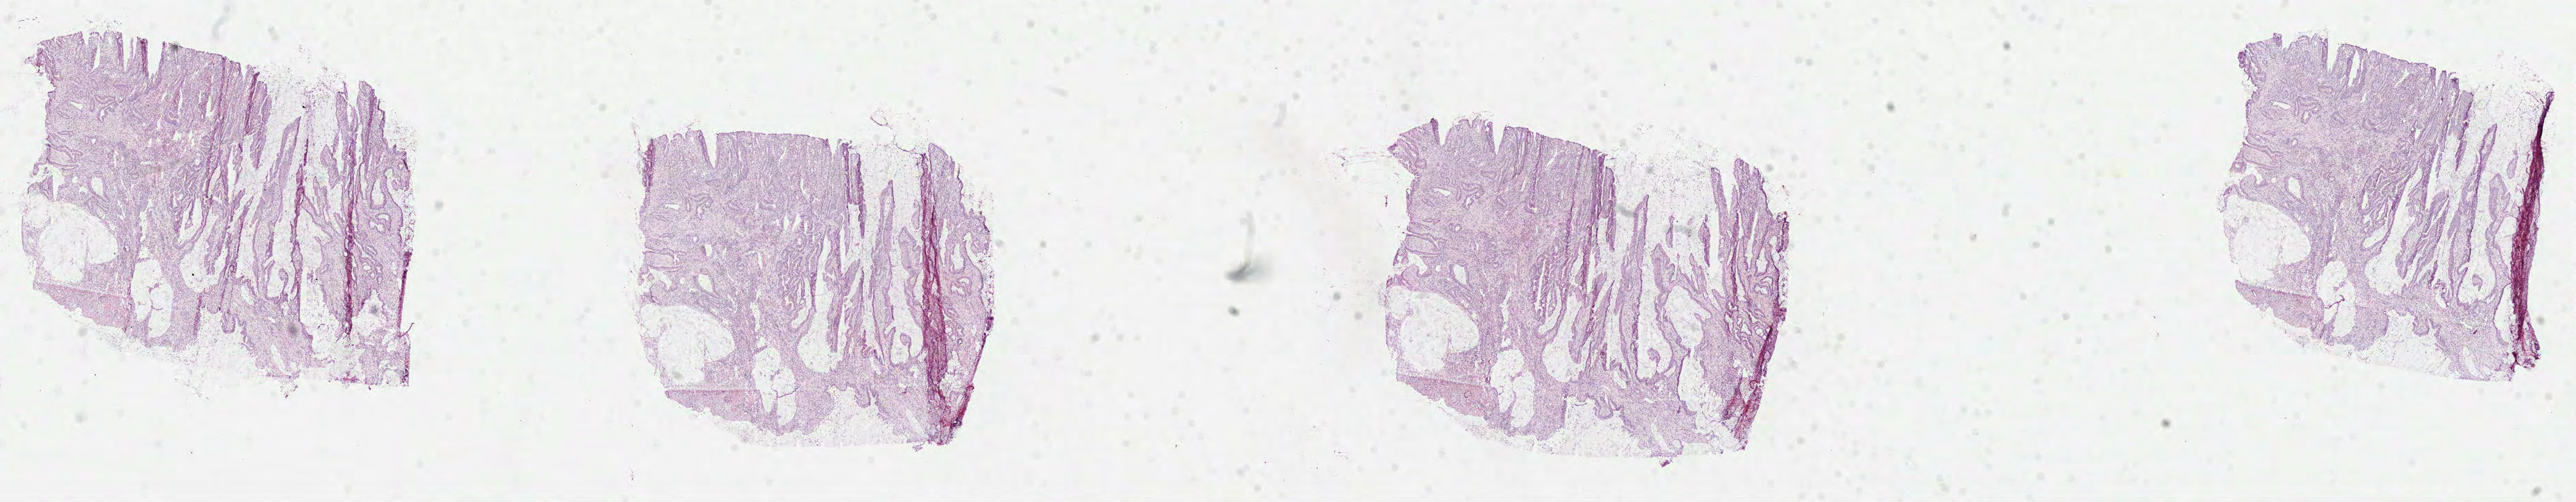
H&E whole-slide image — shown as a low-resolution overview of the whole scanned area (about 30.0 x 5.8 mm, acquisition: 40x scan); formalin-fixed paraffin-embedded (FFPE) diagnostic section; sample: primary tumour, colon. Male, age 67 years at initial diagnosis.
• lymph nodes positive (case pathology): 0 of 20 examined
• AJCC pathologic stage: IIA (7th edition)
• pathologic diagnosis: Mucinous adenocarcinoma